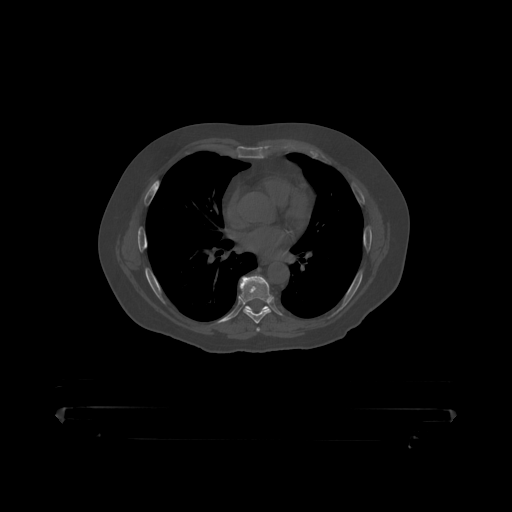
CT including the spine, one axial slice. Slice 274 of 390 in the series (ordered by position). Reconstruction kernel STANDARD. Bone window (W 1800 / L 400 HU). 1.25 mm slice thickness. 512 × 512 image matrix, field of view 650 × 650 mm. Patient: male, 60 years. From the clinical record (not read from this slice): primary cancer: prostate.
Structures marked on this image (semi-automatic segmentation, software-assisted and operator-edited):
- T7 vertebra: bounding box [x1, y1, x2, y2] px = [240, 275, 273, 319]
- T8 vertebra: [245, 306, 270, 311]